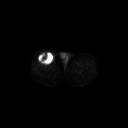
FDG PET of an extremity soft-tissue mass (from a PET/CT study), one axial slice; slice 279 of 311 in the series (ordered by position); 3.27 mm slice thickness; 128 × 128 image matrix, field of view 700 × 700 mm. Patient: male, 56 years. Case-level facts recorded for this patient, not image findings: histological type: pleiomorphic leiomyosarcoma; grade: intermediate; site of the primary tumour: right thigh.
Structures marked on this image (expert contour drawn on MRI and transferred to this co-registered scan by the dataset authors):
- gross tumour volume including surrounding oedema: bounding box (x1, y1, x2, y2) in pixels: (38, 52, 54, 65)
- gross tumour volume (mass): (38, 52, 54, 65)